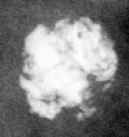
Crop from a digitized film mammogram around one marked abnormality; left breast; CC view; BI-RADS breast density category 3 (scale 1–4).
- Calcifications, distribution linear; BI-RADS assessment category 2; benign without callback (not worked up further).